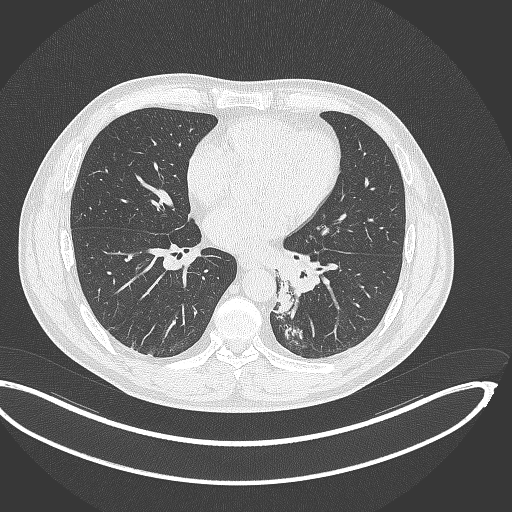
Chest CT, one axial slice; slice 156 of 362 in the series (ordered by position); lung window (W 1500 / L -600 HU); 512 × 512 image matrix, field of view 442 × 442 mm. Male patient, age 50 years. From the clinical record (not read from this slice): clinical TNM (as recorded): T2a N3 M0.
Outlined on this slice (bounding box drawn by a radiologist):
- lung tumour (recorded histology: squamous cell carcinoma): bounding box (x1, y1, x2, y2) in pixels: (272, 276, 296, 317)